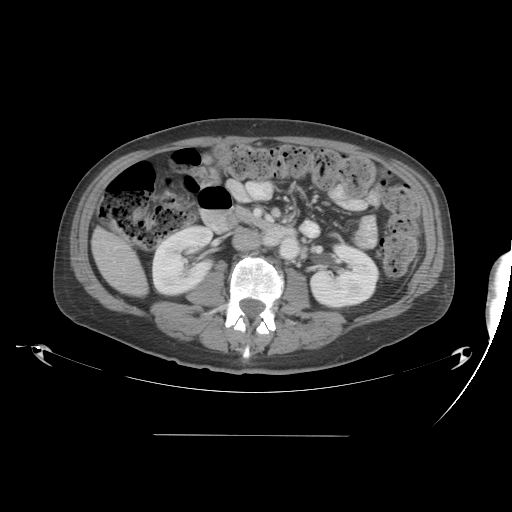
Contrast-enhanced abdominal CT, one axial slice. 120 kVp. Intravenous contrast given. Soft-tissue window (W 400 / L 40 HU). 512 × 512 image matrix, field of view 486 × 486 mm. Male patient, age 65 years. From the clinical record (not read from this slice): diagnosis: colorectal cancer liver metastases, imaged before liver resection; multiple liver metastases: yes; largest metastasis: 11 cm; disease in both lobes: yes.
Annotated regions visible in this slice (outlined manually by an expert reader):
- liver: bounding box [x1, y1, x2, y2] px = [94, 230, 147, 296]